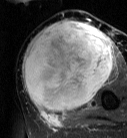
MRI of an extremity soft-tissue mass, one axial slice. Slice 34 of 87 in the series (ordered by position). T2-weighted fat-saturated. MR volume resampled by the dataset authors to the PET/CT grid (not the native acquisition matrix). 3.27 mm slice thickness. 127 × 138 image matrix, field of view 124 × 135 mm. Female patient. Case-level facts recorded for this patient, not image findings: histological type: pleiomorphic leiomyosarcoma; grade: high; site of the primary tumour: left biceps.
Outlined on this slice (expert contour drawn on MRI and transferred to this co-registered scan by the dataset authors):
- gross tumour volume including surrounding oedema: bounding box <22,20,114,113> (left, top, right, bottom; pixels)
- gross tumour volume (mass): <22,21,114,113>